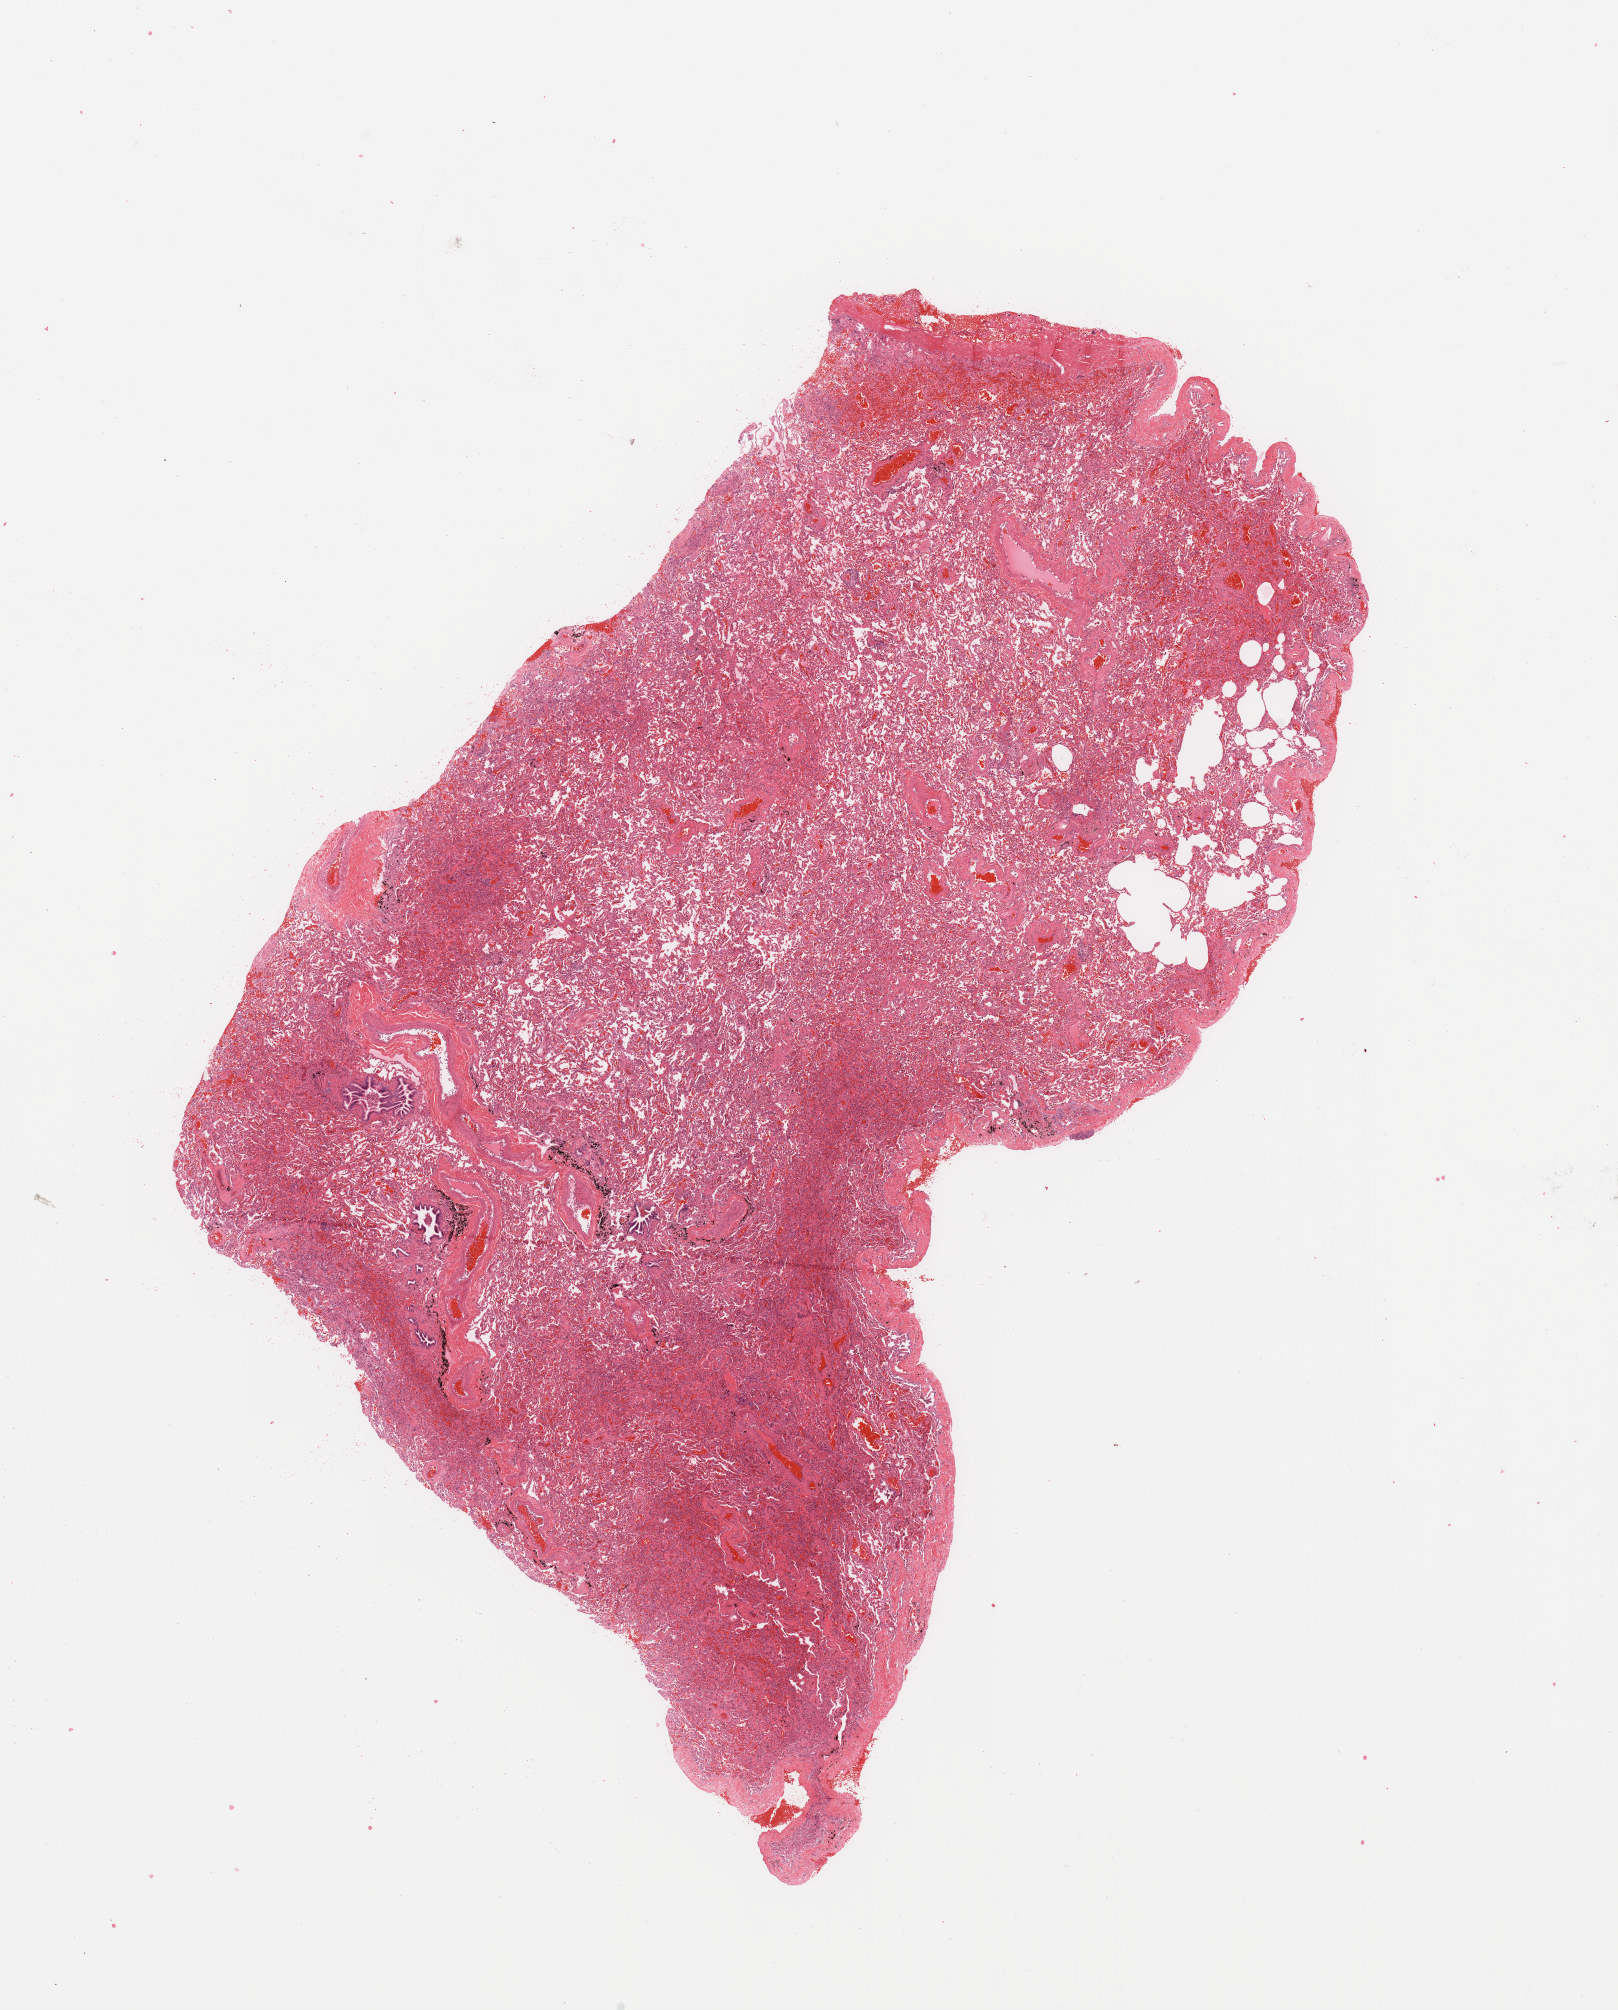
Digitized H&E tissue section (whole slide), shown as a low-resolution overview of the whole scanned area (about 12.8 x 15.9 mm, acquisition: 20x scan), normal (non-tumour) tissue sample, sampled site: lung. 44-year-old female patient.
This section: normal (non-tumour) tissue from the same patient. Patient diagnosis: Adenocarcinoma, NOS.